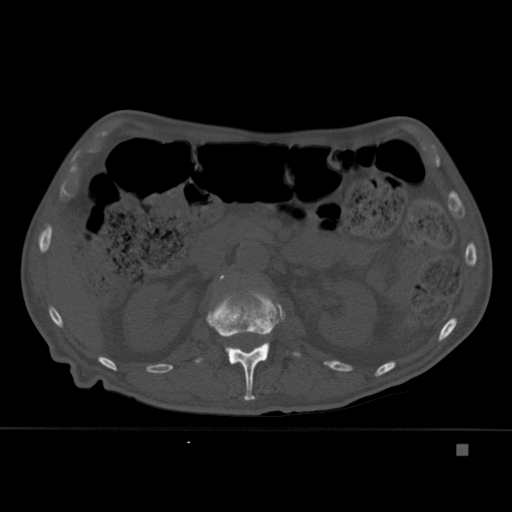
CT including the spine, one axial slice; position 178 of 451 along the scan axis; bone window (W 1800 / L 400 HU); 512 × 512 image matrix. Male patient, age 75 years. From the clinical record (not read from this slice): primary cancer: prostate.
Annotated regions visible in this slice (semi-automatic segmentation, software-assisted and operator-edited):
- L1 vertebra: bounding box [x1, y1, x2, y2] px = [195, 288, 301, 401]
- L2 vertebra: [220, 275, 225, 281]